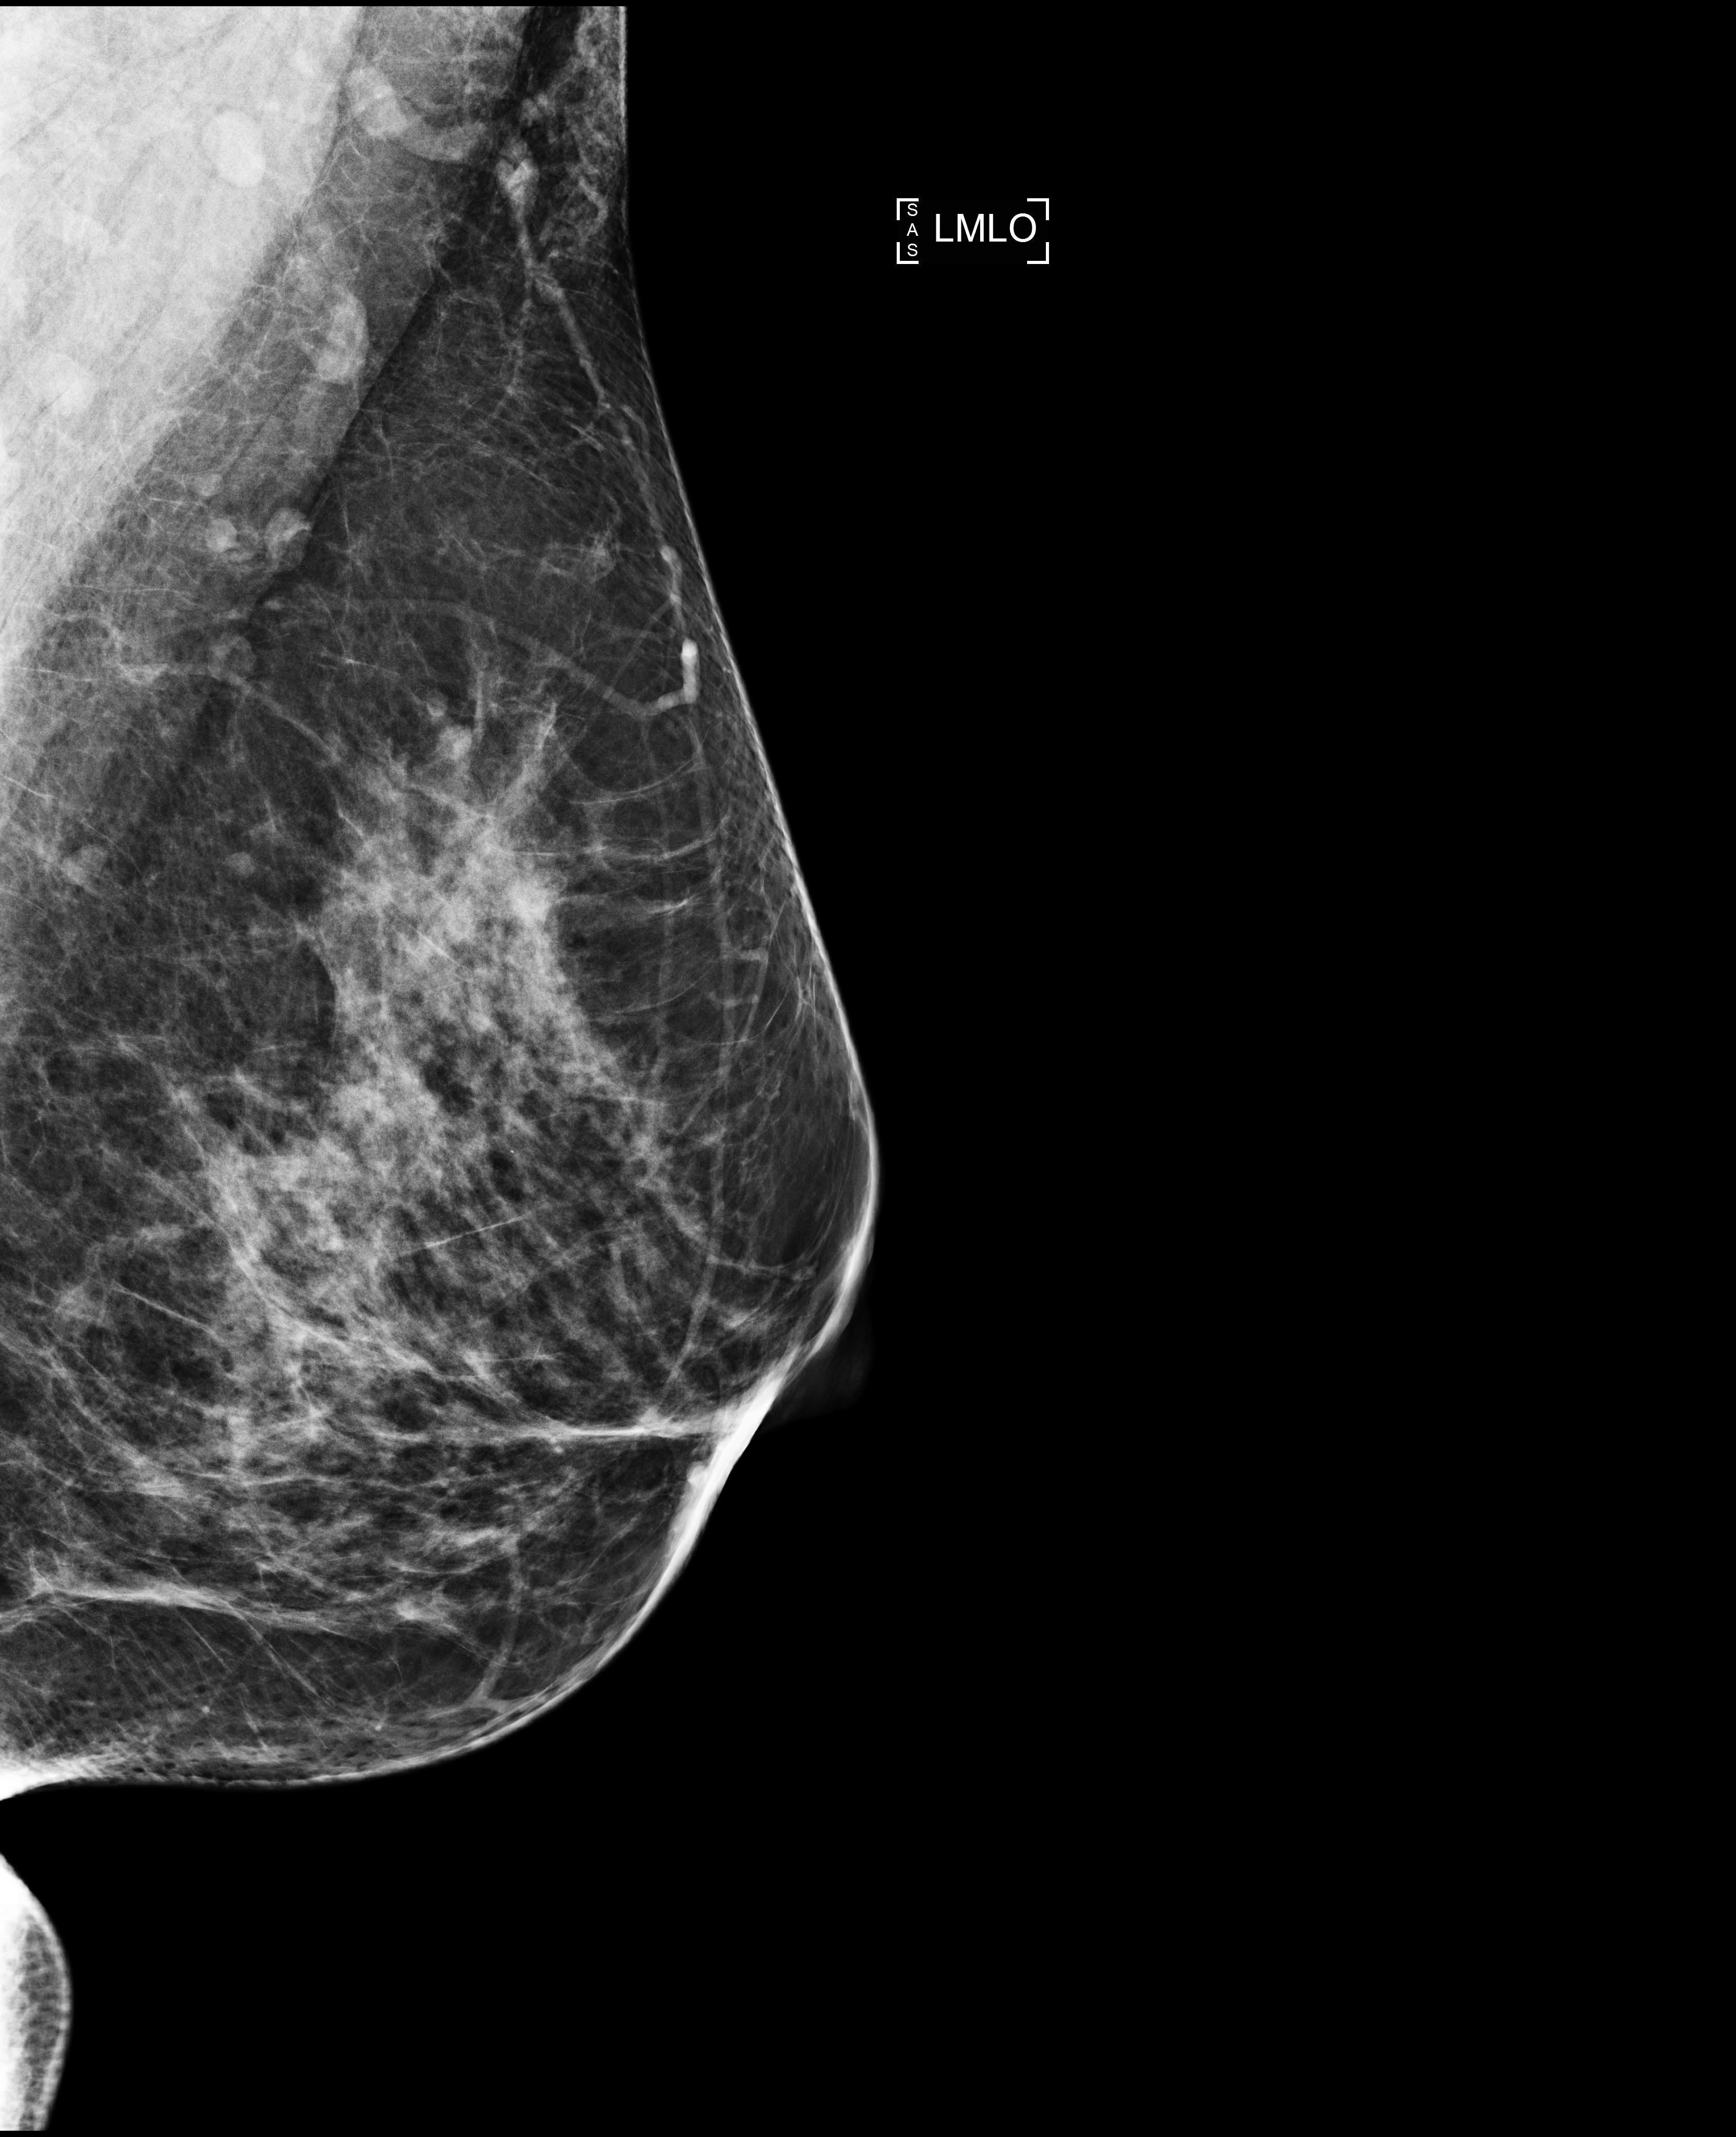
Screening examination, compressed breast thickness 65 mm. Patient: female, 45 years.
Image type: full-field digital mammogram. Breast: left. Projection: MLO view.